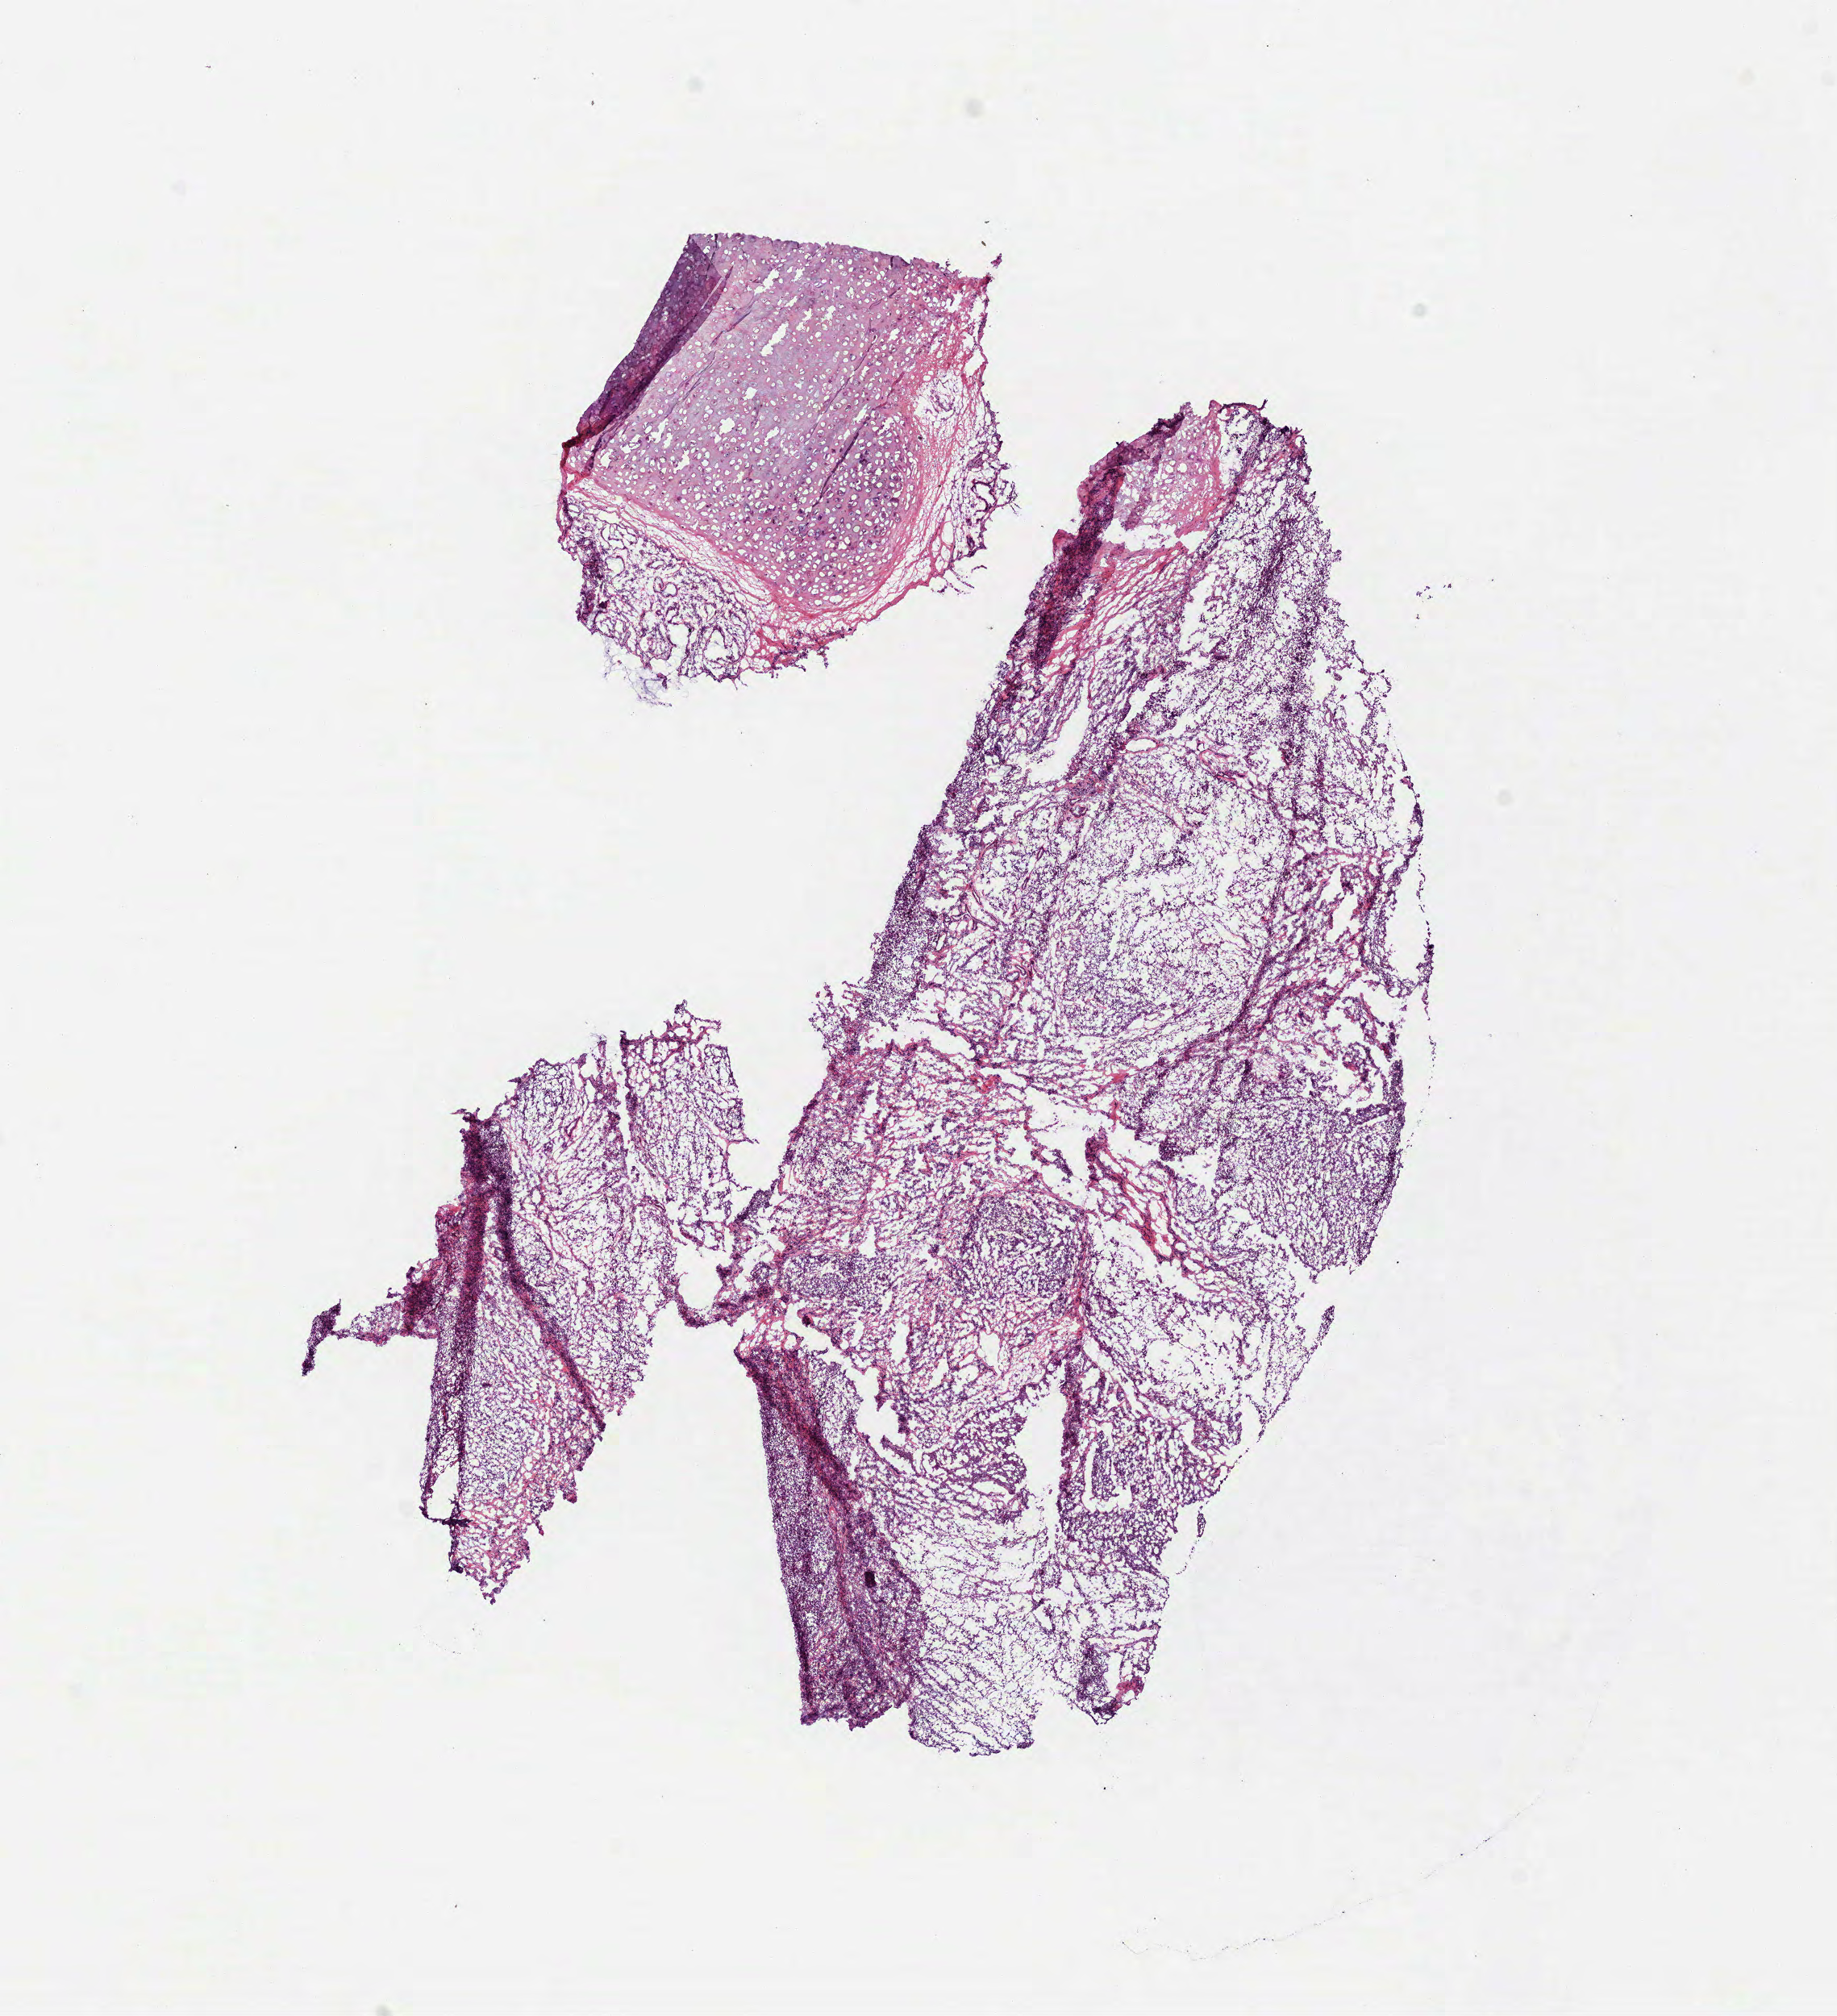
H&E whole-slide image — shown as a low-resolution overview of the whole scanned area (about 9.2 x 10.1 mm, slide scanned at 40x); frozen section from the bottom of the tissue portion; sample: primary tumour, head and neck. Patient: male, age at initial diagnosis 60 years. Histologic grade: G3 (poorly differentiated). Pathologist review of this section (percent, as recorded): tumour cells 80%, tumour nuclei 80%, normal cells 20%, stromal cells 0%, necrosis 0%. Inflammatory infiltration, as recorded: lymphocyte infiltration 3%, monocyte infiltration 0%, neutrophil infiltration 0%.
- diagnosis: Squamous cell carcinoma, NOS (tongue, NOS)
- lymph nodes positive (case pathology): 2 of 12 examined
- AJCC pathologic stage: IVA (7th edition)